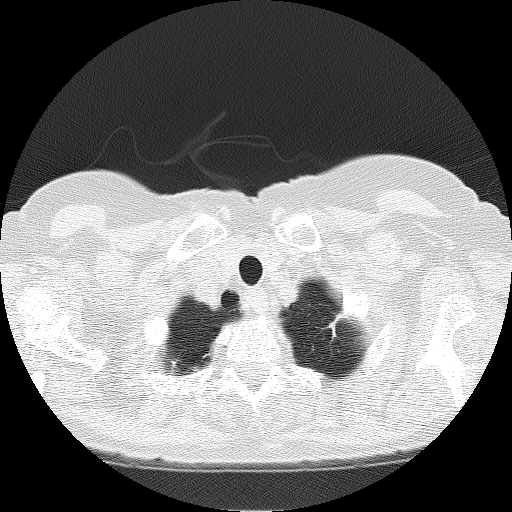
Low-dose screening chest CT, one axial slice; position 157 of 166 along the scan axis; lung window (W 1500 / L -600 HU); 2 mm slice thickness; 512 × 512 image matrix, field of view 303 × 303 mm.
Annotated regions visible in this slice (manually delineated by an expert):
- lesion 3 (nodule, upper lobe of left lung): bounding box [x1, y1, x2, y2] px = [331, 324, 333, 327]